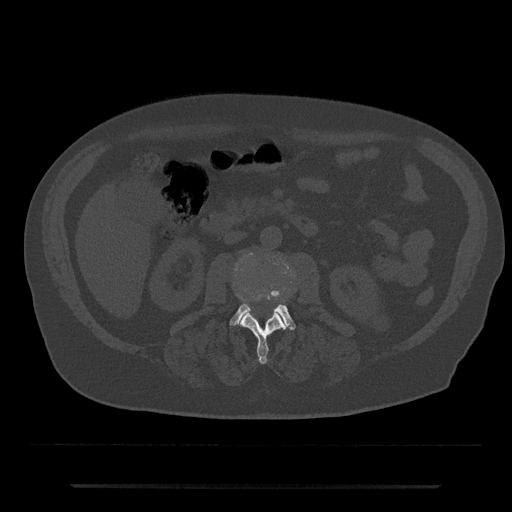
CT including the spine, one axial slice. Reconstruction kernel Br40s/3. Bone window (W 1800 / L 400 HU). 0.5 mm slice thickness. 512 × 512 image matrix, field of view 434 × 434 mm. Patient: male, 80 years. Case-level facts recorded for this patient, not image findings: primary cancer: prostate.
Annotated regions visible in this slice (semi-automatically segmented with operator editing):
- L2 vertebra: bounding box [x1, y1, x2, y2] px = [240, 295, 288, 364]
- L3 vertebra: [230, 290, 296, 330]